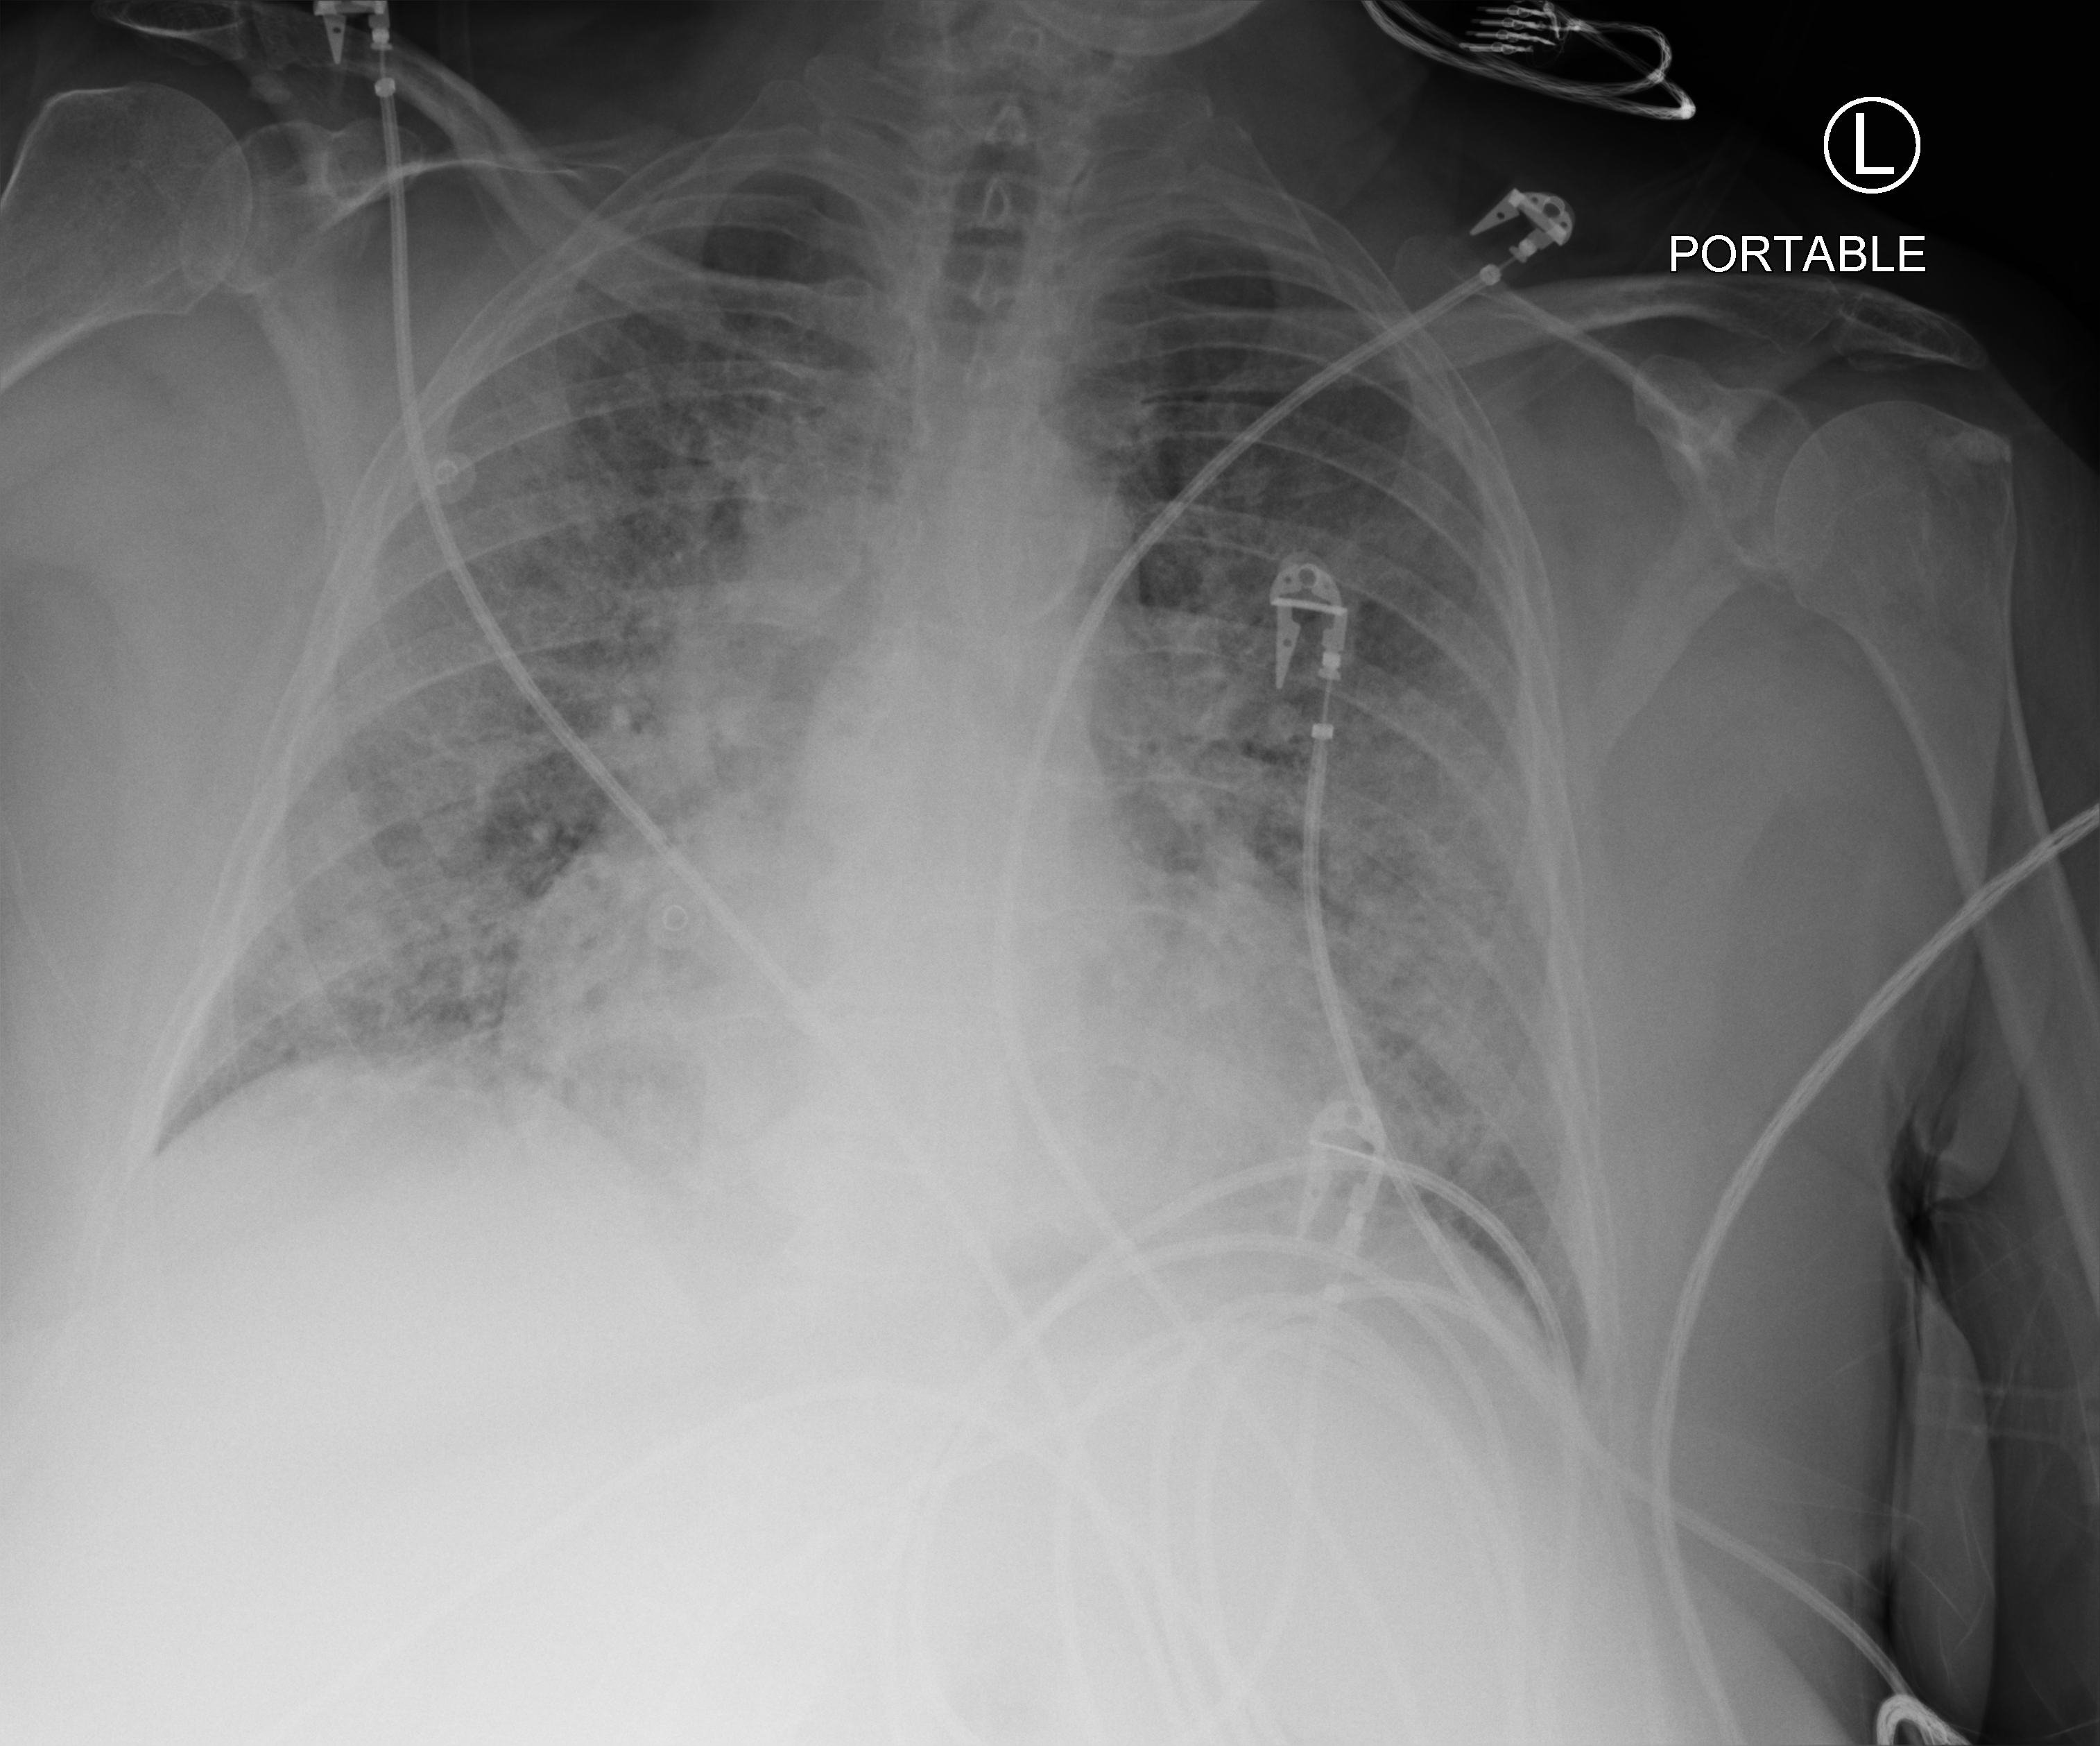
Portable chest radiograph, anteroposterior (AP) projection. Female patient hospitalised with COVID-19, age 75–90 years.
Admission-level facts for this patient (not findings on this image; timing relative to this image not recorded): admitted to intensive care during this hospital stay: yes; length of hospital stay: 31 days.